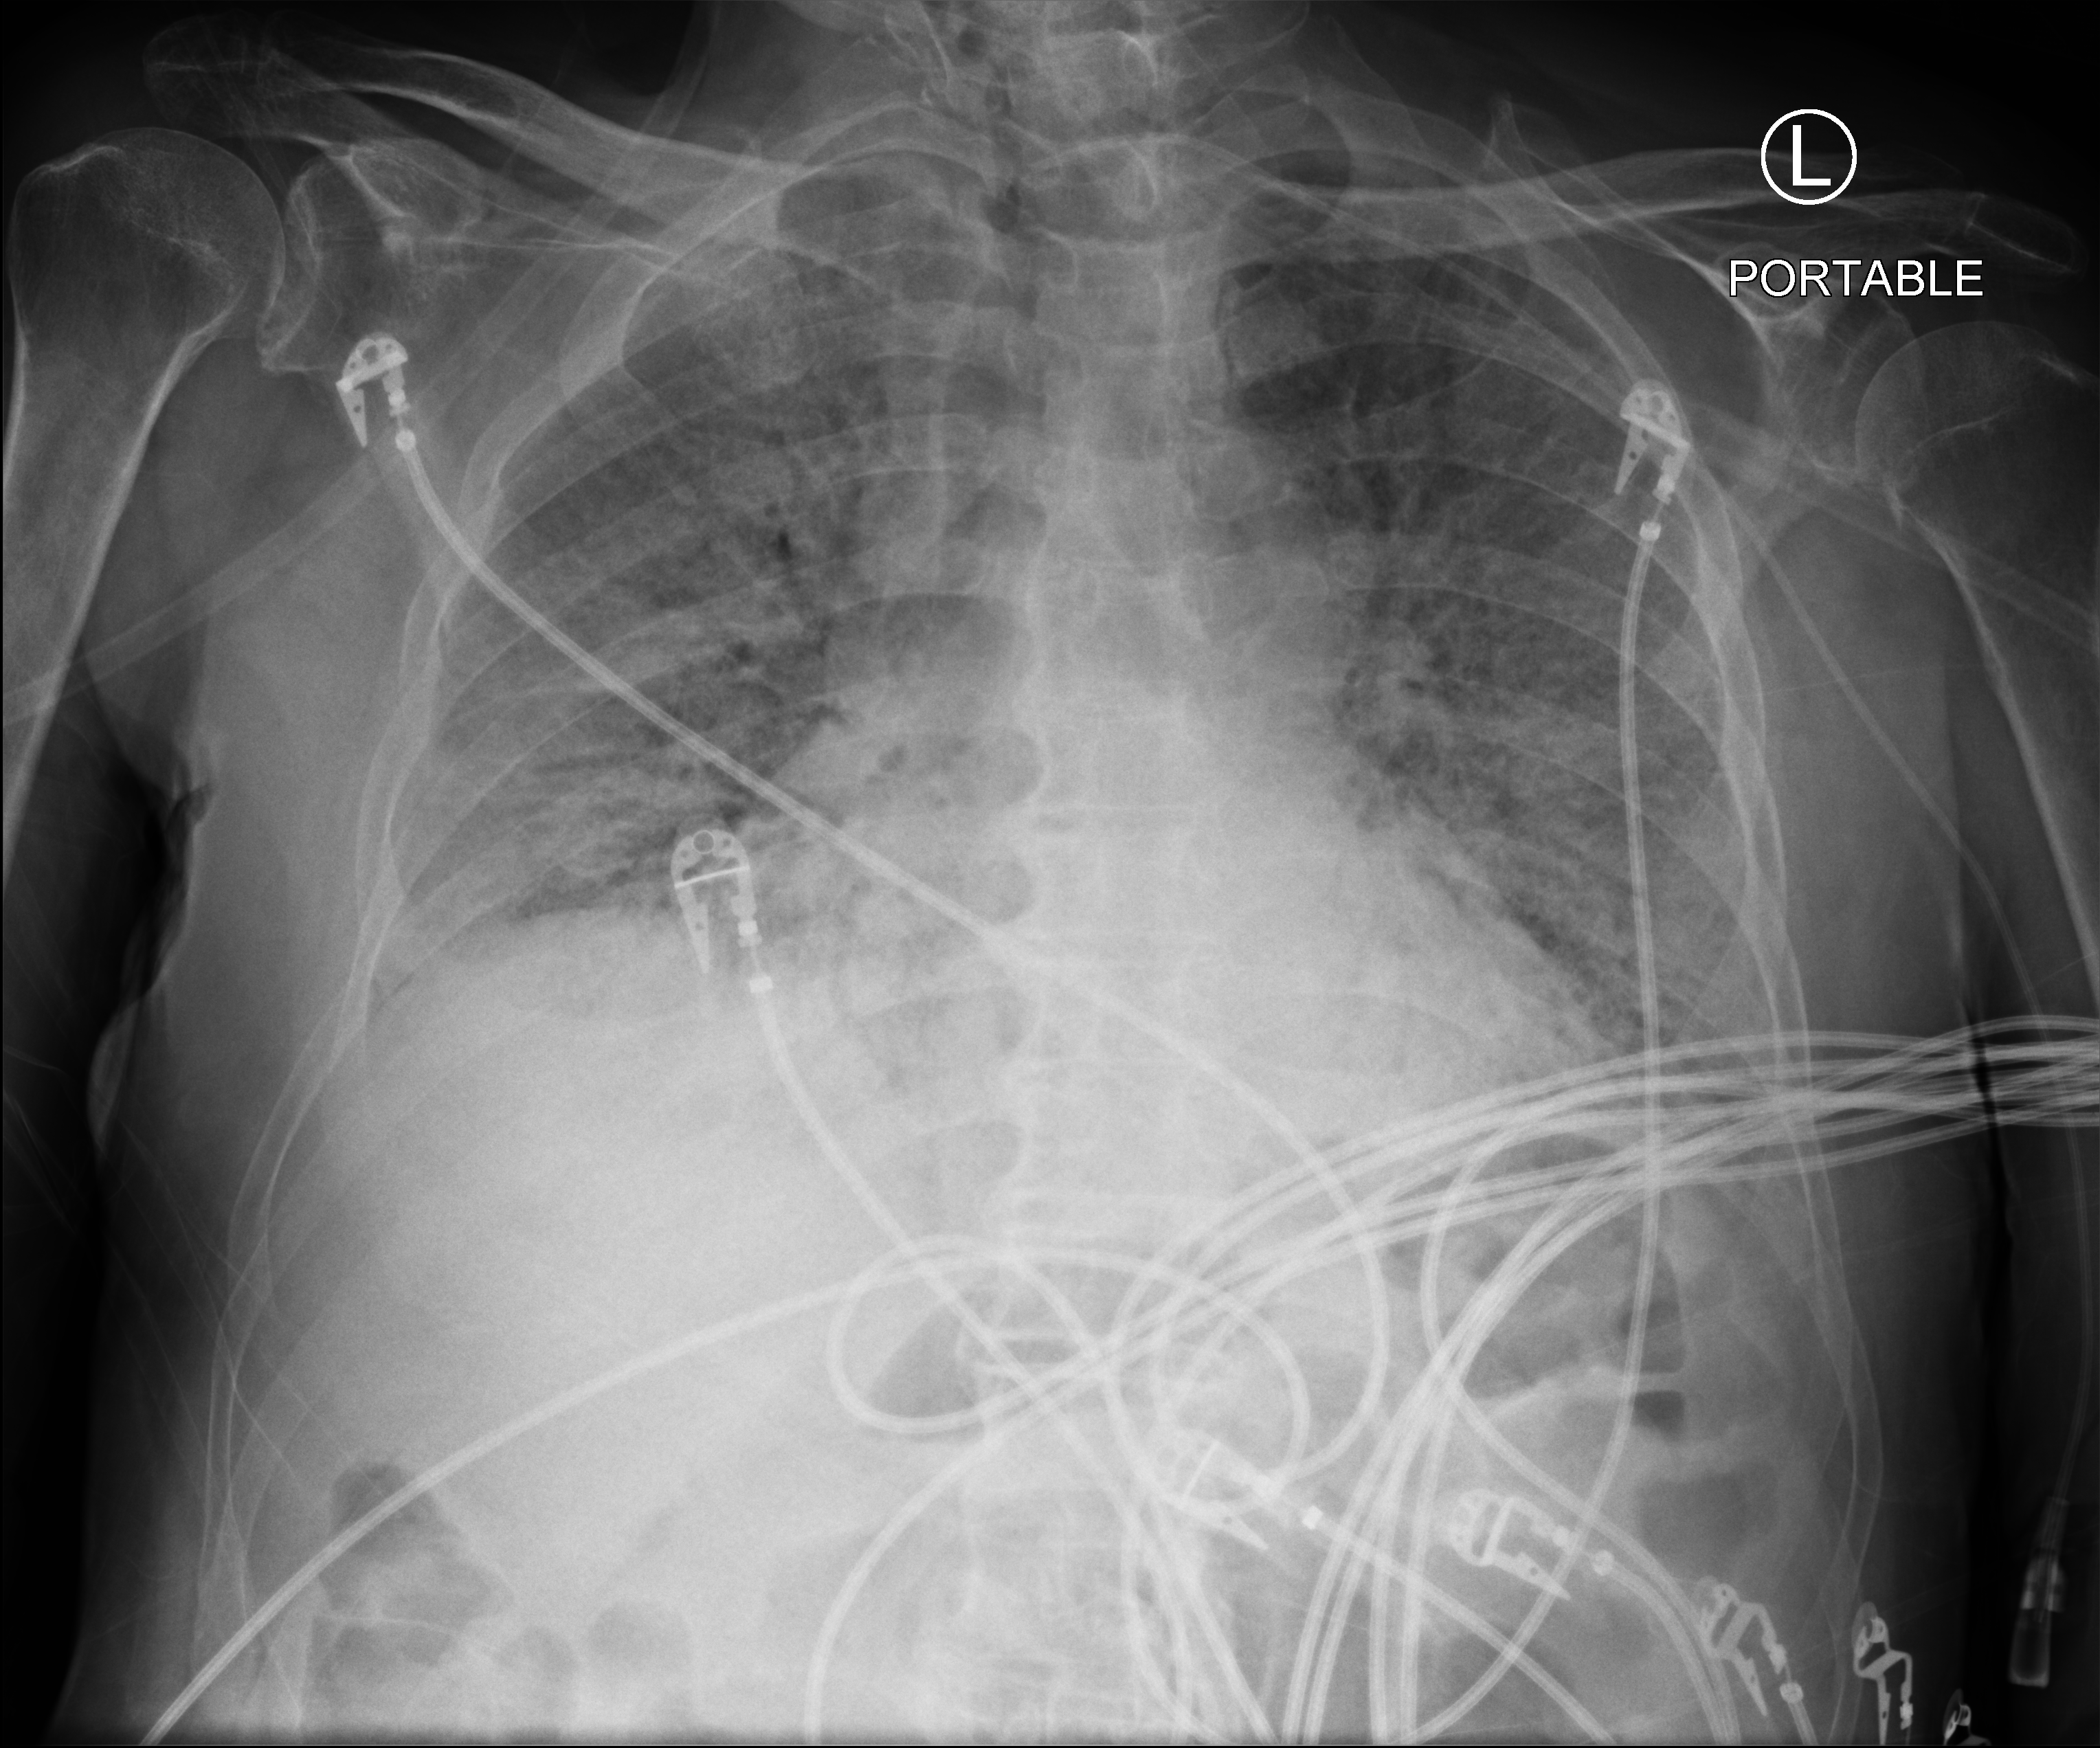
Chest X-ray (portable); anteroposterior (AP) projection. Patient hospitalised with COVID-19; male, aged 75–90 years.
Admission-level facts for this patient (not findings on this image; timing relative to this image not recorded):
- mechanically ventilated during this hospital stay: yes
- admitted to intensive care during this hospital stay: yes
- COPD (admission record): no